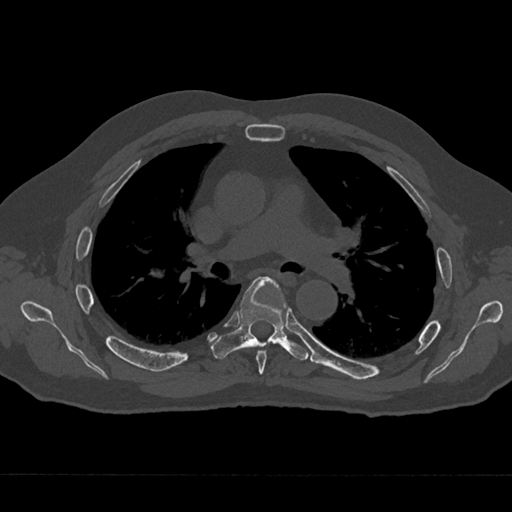
CT including the spine, one axial slice. Reconstruction kernel Br40s/3. 120 kVp. Bone window (W 1800 / L 400 HU). 512 × 512 image matrix. Male patient, age 75 years. From the clinical record (not read from this slice): primary cancer: renal; vertebrae with lytic lesions (as recorded): T4.
Annotated regions visible in this slice (semi-automatically segmented with operator editing):
- T5 vertebra: box from (x=256, y=302) to (x=284, y=374) px
- T6 vertebra: (x=212, y=276)–(x=309, y=360)